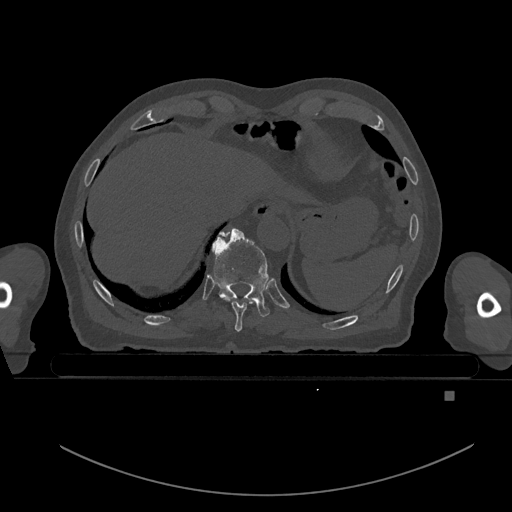
CT including the spine, one axial slice; bone window (W 1800 / L 400 HU); 0.5 mm slice thickness; 512 × 512 image matrix. Male patient, age 82 years. From the clinical record (not read from this slice): primary cancer: prostate; vertebrae with lytic lesions (as recorded): T11, T9, T8, T2.
Structures marked on this image (semi-automatically segmented with operator editing):
- T10 vertebra: box from (x=211, y=228) to (x=270, y=317) px
- T9 vertebra: (x=219, y=232)–(x=252, y=332)